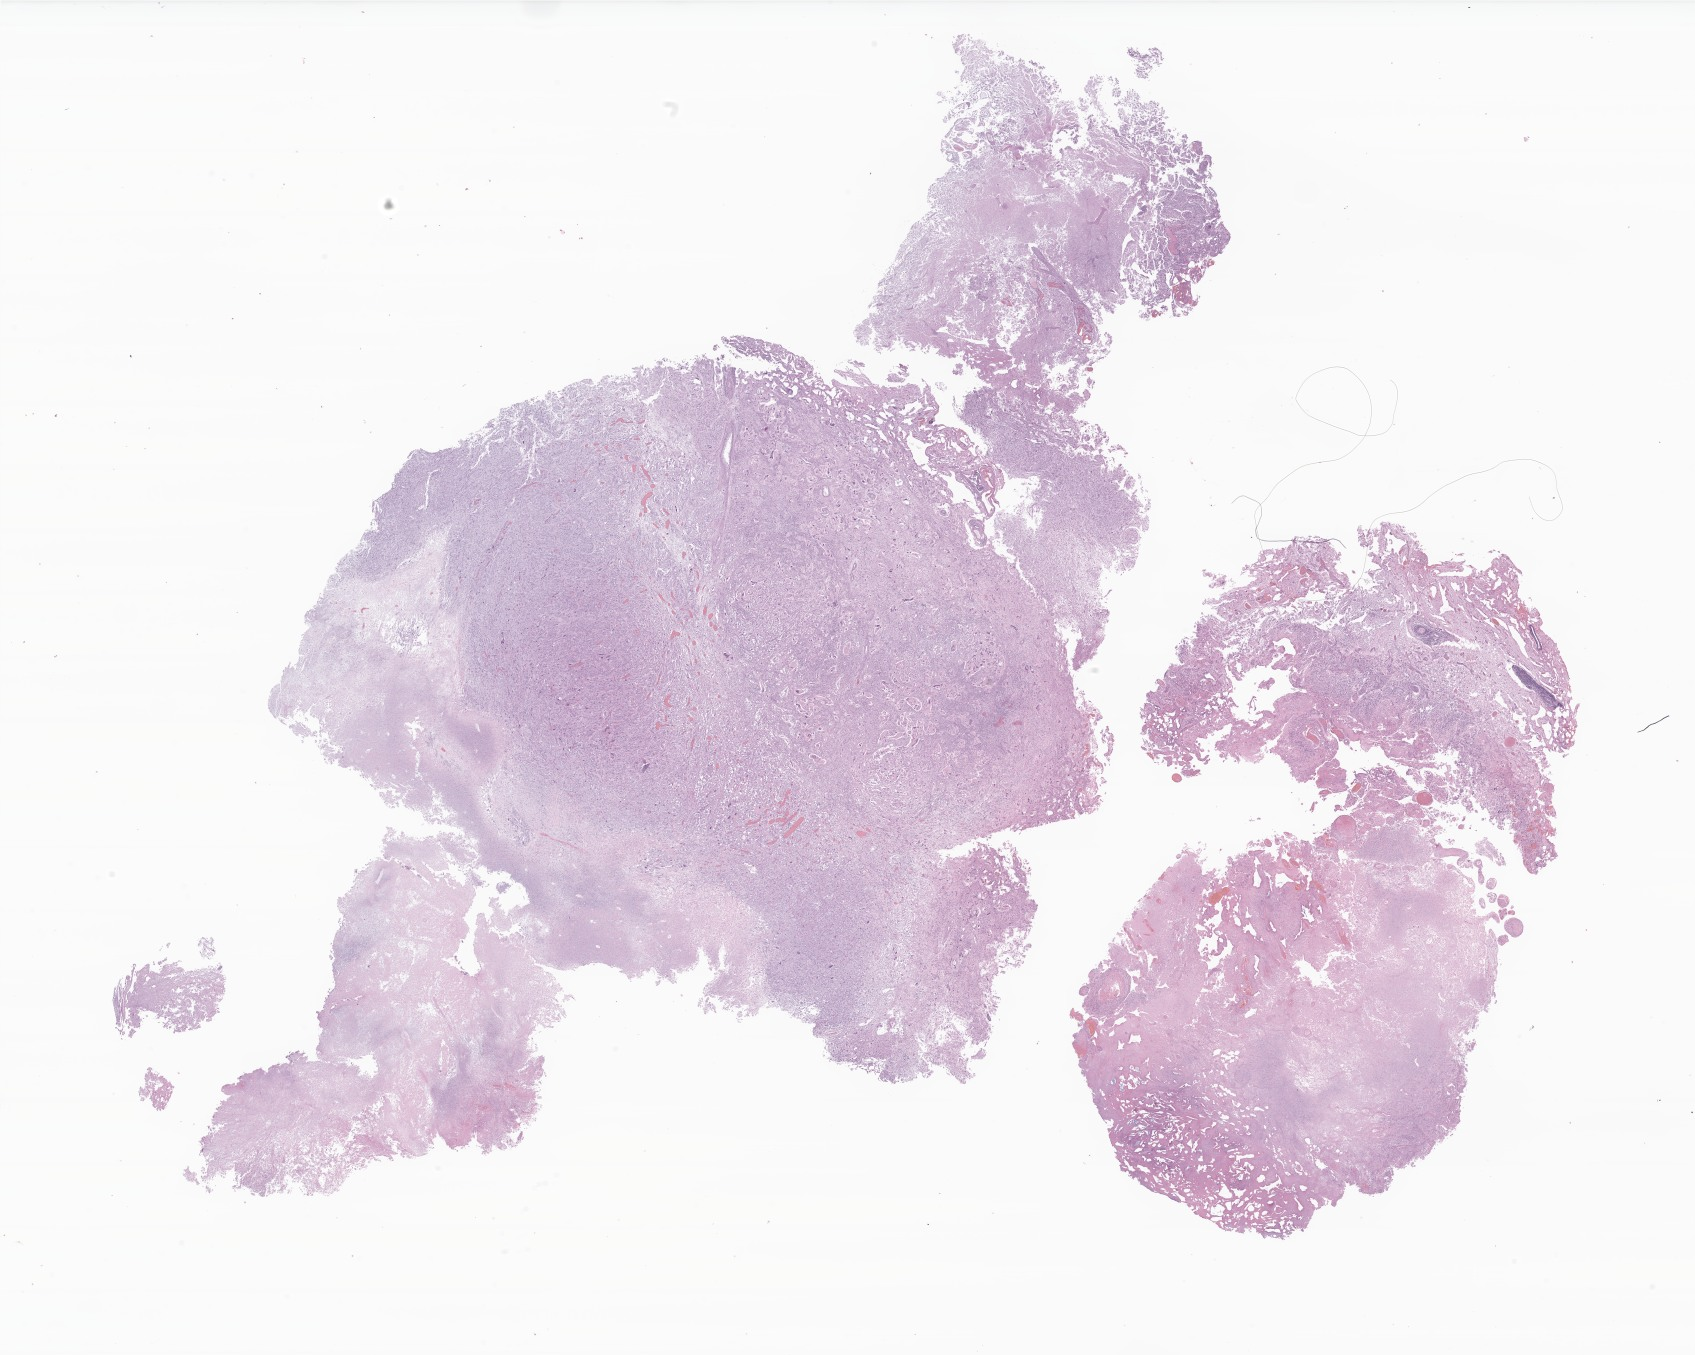
Digitized hematoxylin and eosin (H&E)-stained section of tumor tissue from the frontal lobe — whole scanned area (about 28.6 x 22.9 mm) shown as a low-resolution overview, FFPE section. Male patient, age 207 months (17 years 3 months).
• diagnosis: Glioblastoma, NOS